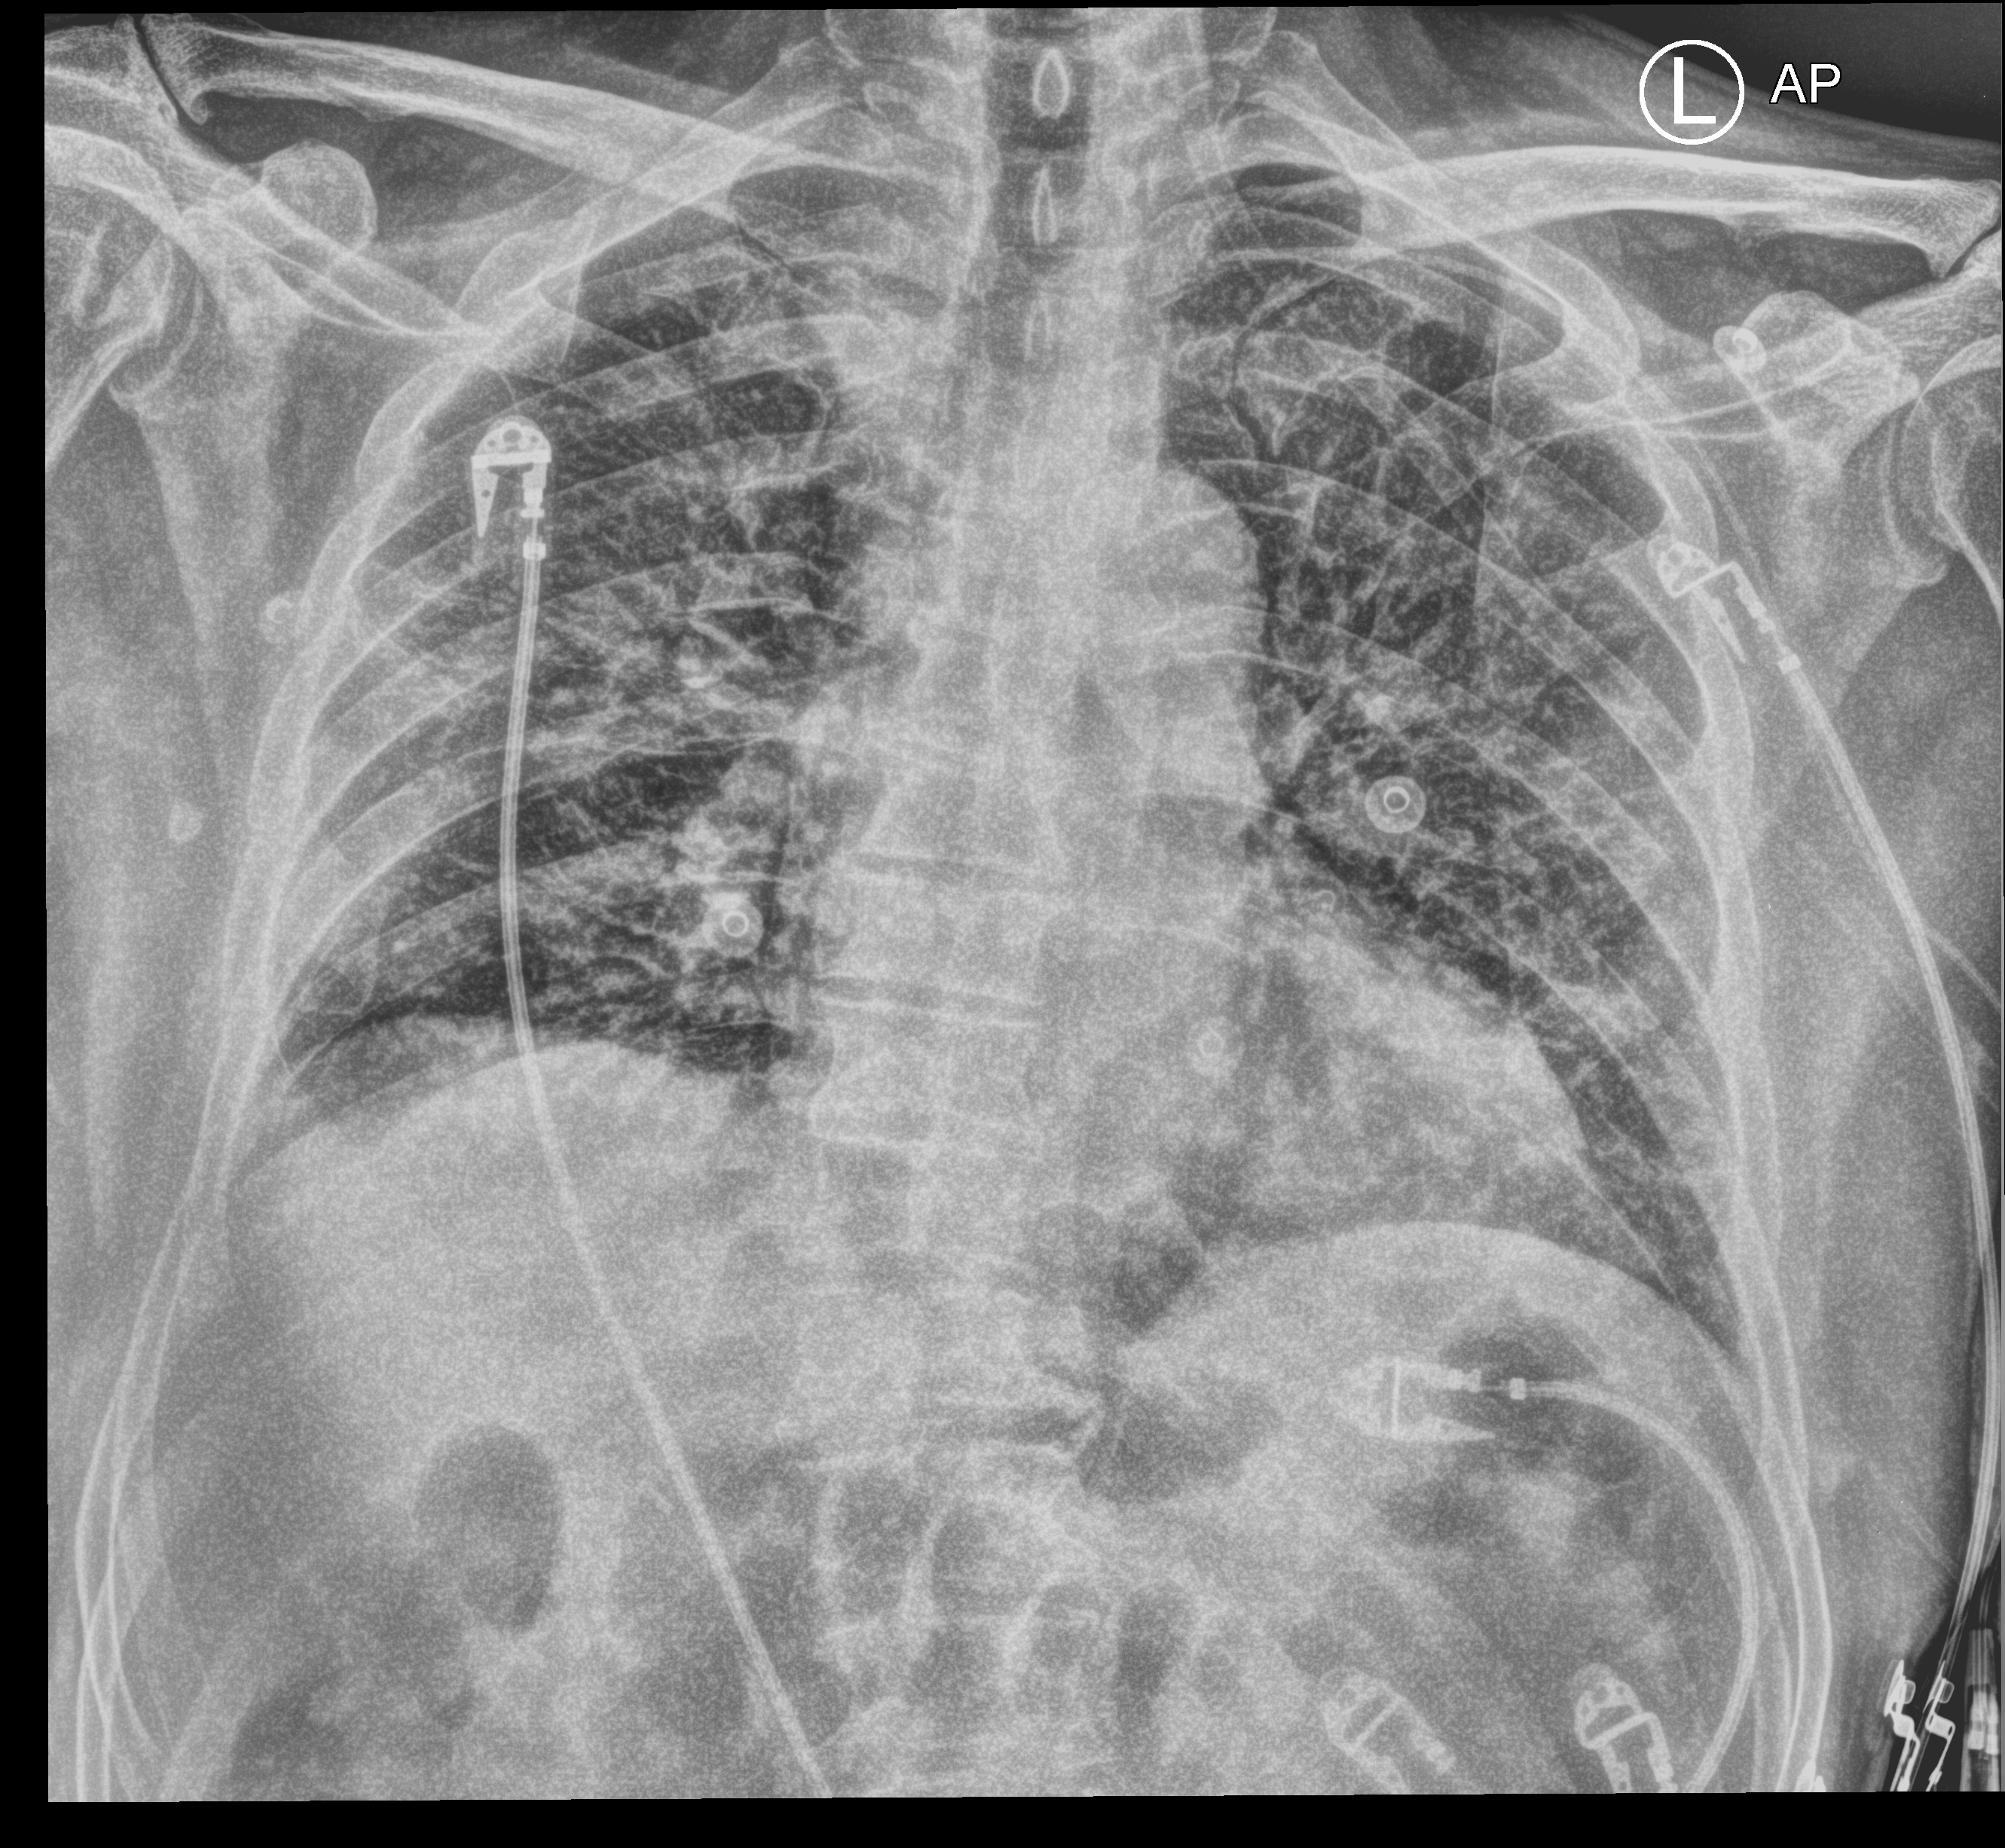
Chest X-ray (portable), anteroposterior (AP) projection. Patient hospitalised with COVID-19; male, aged 60–74 years.
Admission-level facts for this patient (not findings on this image; timing relative to this image not recorded): mechanically ventilated during this hospital stay: no.